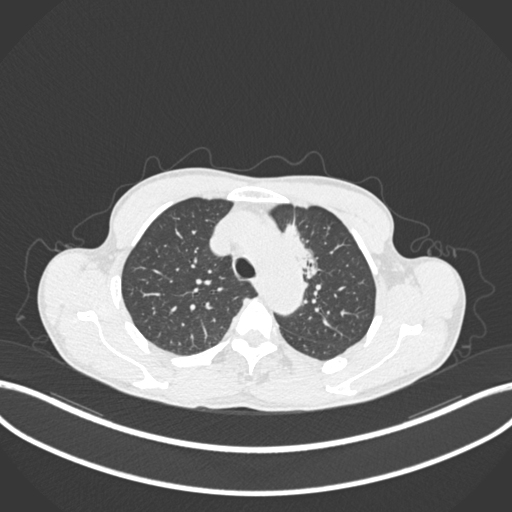
Chest CT, one axial slice. Position 153 of 211 along the scan axis. Reconstruction kernel B30f. 120 kVp. Lung window (W 1500 / L -600 HU). 1 mm slice thickness. 512 × 512 image matrix. Male patient, age 58 years. From the clinical record (not read from this slice): clinical TNM (as recorded): T1c N1 M0.
Structures marked on this image (rectangle marked by the reading radiologist):
- lung tumour (recorded histology: adenocarcinoma): bounding box <269,218,325,285> (left, top, right, bottom; pixels)